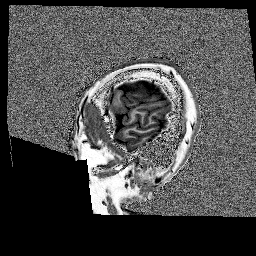
Brain MRI from a brain-tumour surgery series, one sagittal slice; position 27 of 176 along the scan axis; 256 × 256 image matrix, field of view 256 × 256 mm. From the clinical record (not read from this slice): histopathology: Glioblastoma; WHO grade: 4.
Annotated regions visible in this slice (outlined manually by an expert reader):
- tumour: bounding box (x1, y1, x2, y2) in pixels: (118, 80, 175, 98)